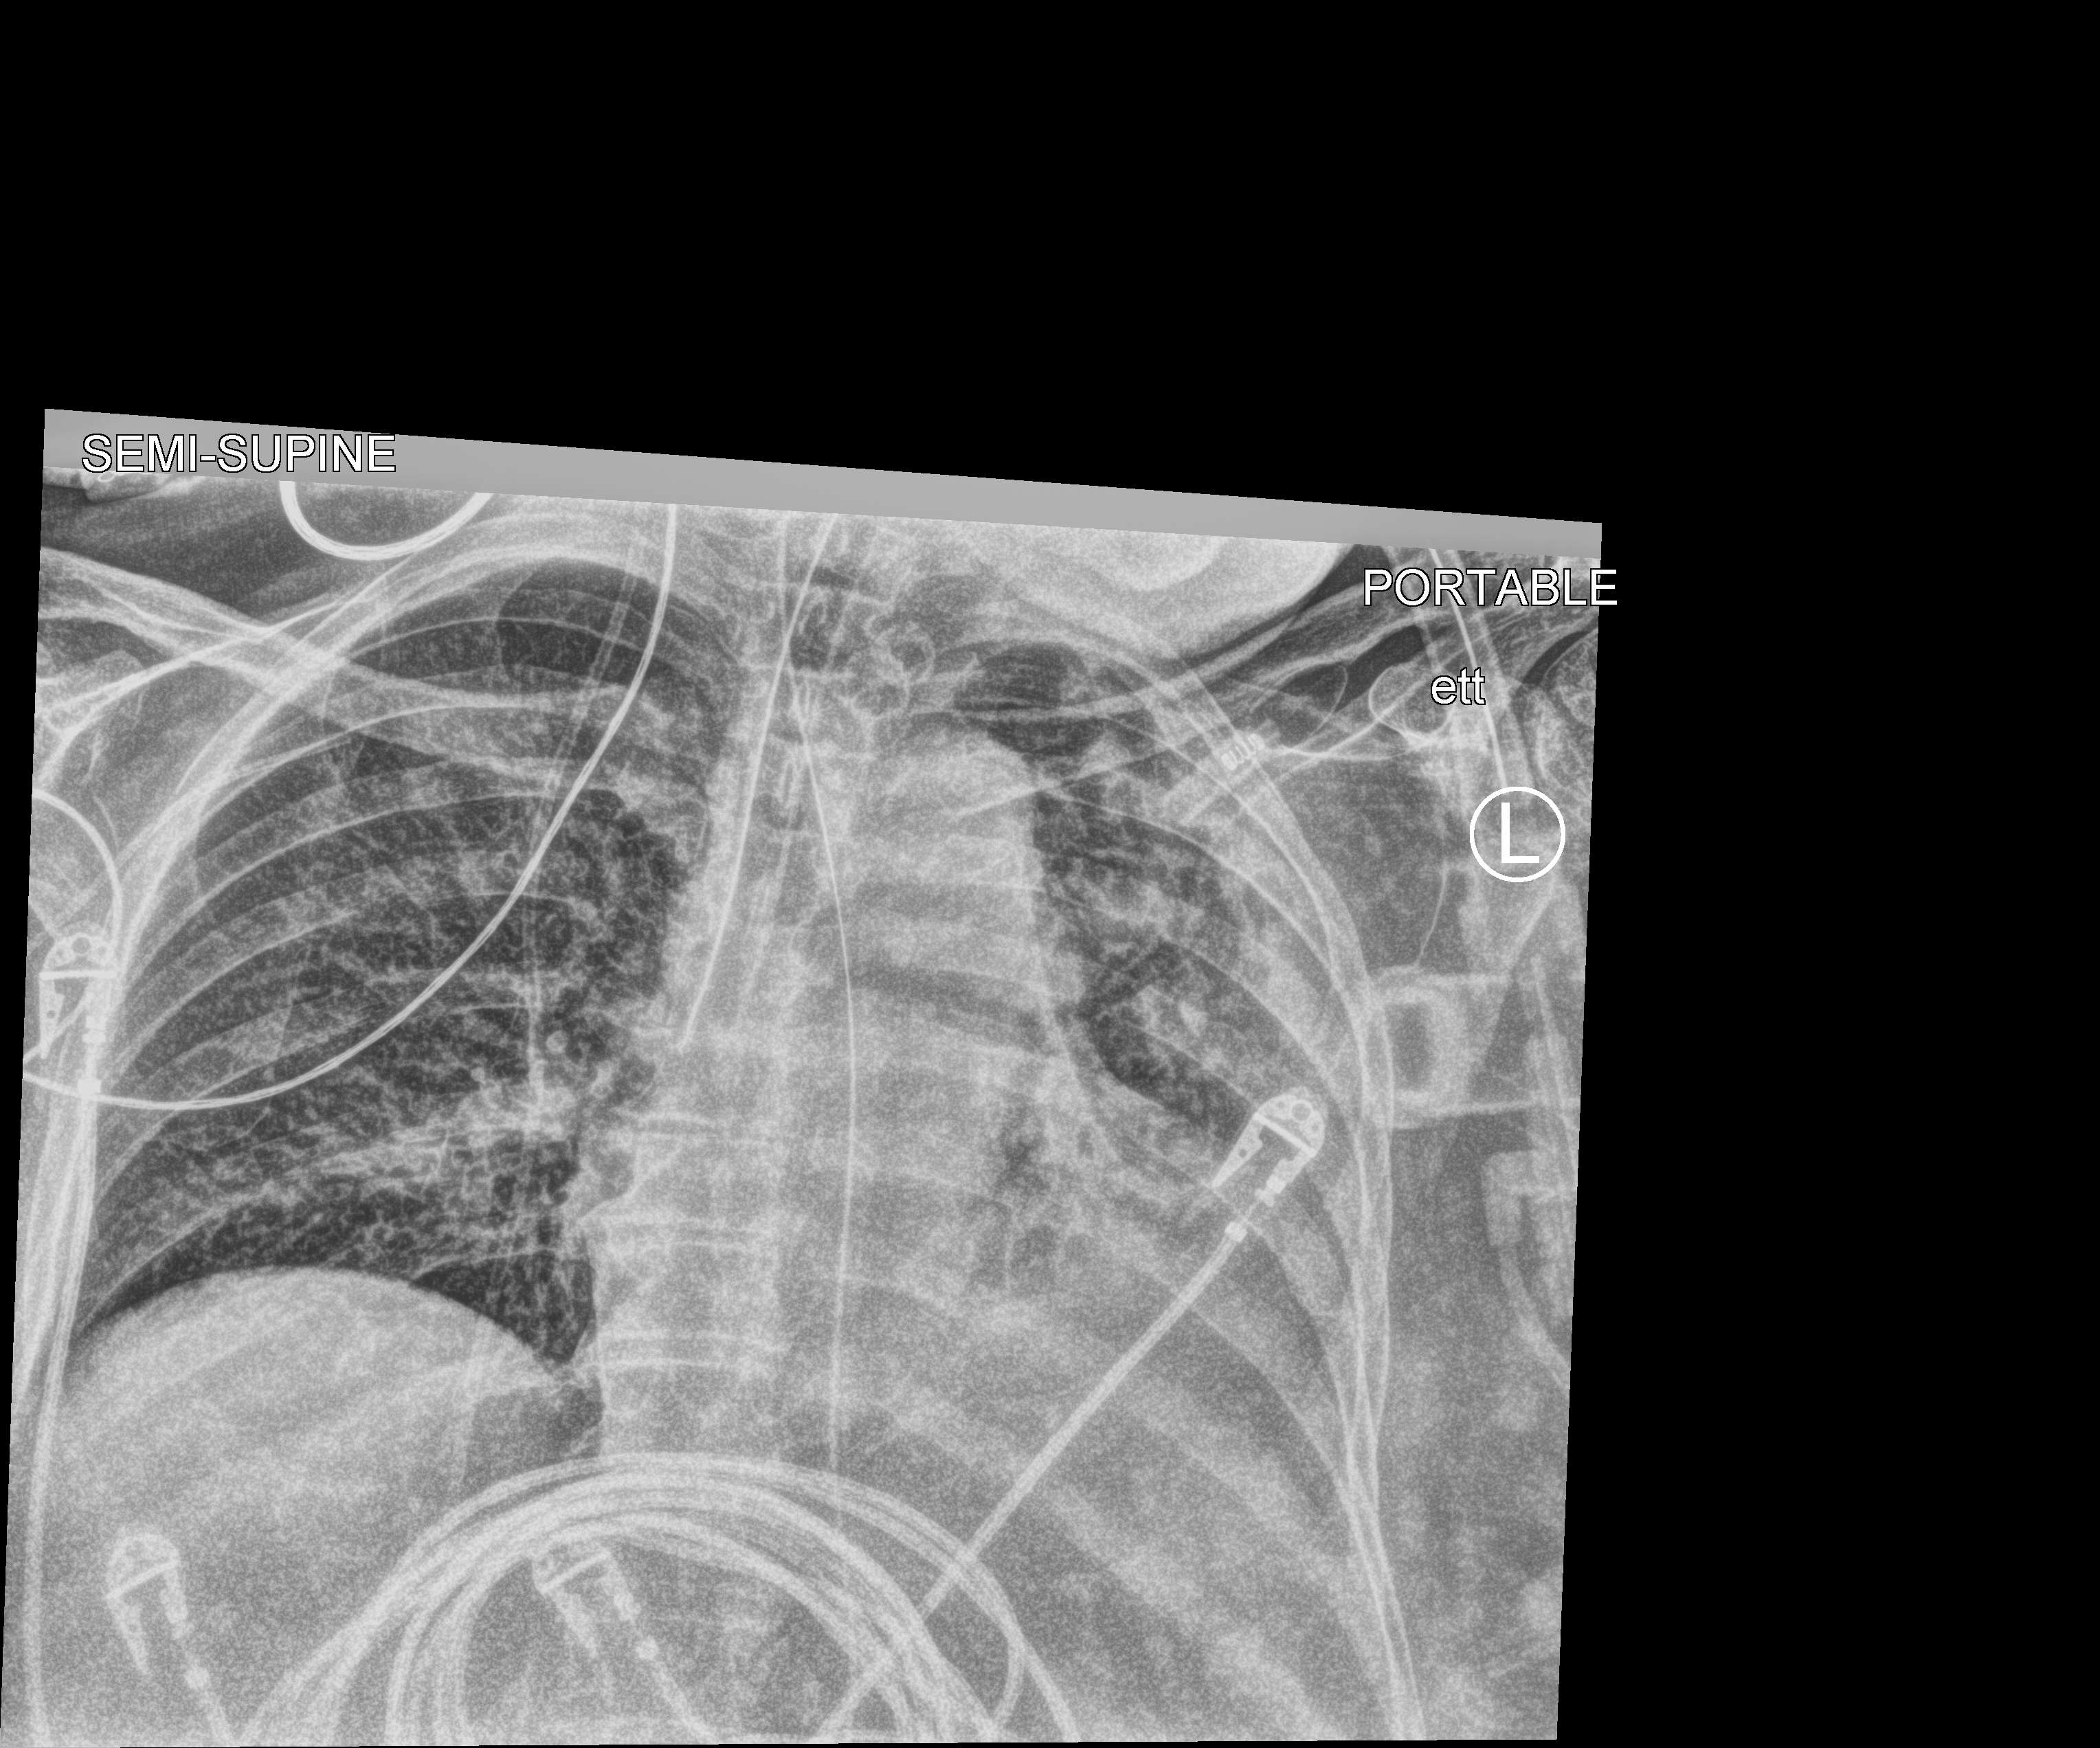
Bedside chest radiograph (computed radiography). Female patient hospitalised with COVID-19, age 75–90 years.
Hospital-stay facts (about this admission, not read from this image; timing relative to this image not recorded): other chronic lung disease (admission record): no; mechanically ventilated during this hospital stay: yes.